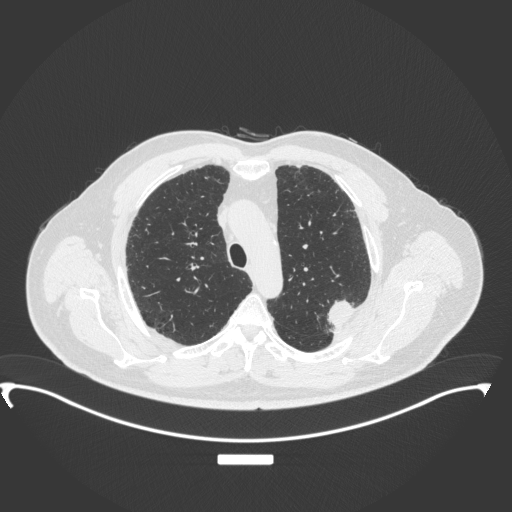
Chest CT, one axial slice; reconstruction kernel B31f; lung window (W 1500 / L -600 HU); 1 mm slice thickness; 512 × 512 image matrix, field of view 459 × 459 mm. Male patient, age 64 years. From the clinical record (not read from this slice): clinical TNM (as recorded): T1c N1 M1.
Annotated regions visible in this slice (rectangle marked by the reading radiologist):
- lung tumour (recorded histology: adenocarcinoma): box from (x=329, y=298) to (x=363, y=336) px